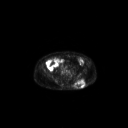
FDG PET of an extremity soft-tissue mass (from a PET/CT study), one axial slice; slice 87 of 267 in the series (ordered by position); 3.27 mm slice thickness; 128 × 128 image matrix. Male patient, age 69 years. Case-level facts recorded for this patient, not image findings: histological type: leiomyosarcoma; grade: intermediate; site of the primary tumour: left pelvis.
Outlined on this slice (expert contour drawn on MRI and transferred to this co-registered scan by the dataset authors):
- gross tumour volume (mass): bounding box (x1, y1, x2, y2) in pixels: (74, 79, 86, 88)